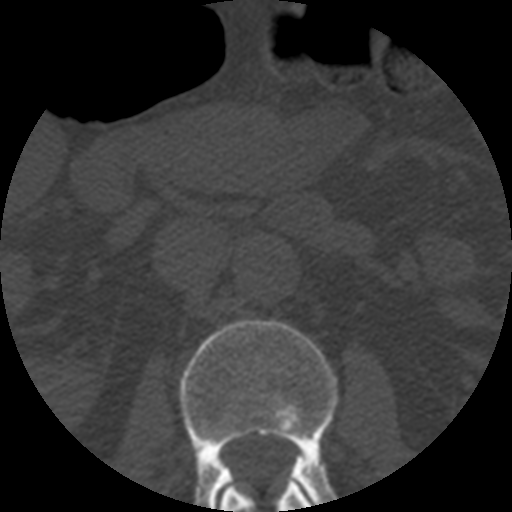
CT including the spine, one axial slice; slice 162 of 508 in the series (ordered by position); reconstruction kernel STANDARD; bone window (W 1800 / L 400 HU); 1.25 mm slice thickness; 512 × 512 image matrix, field of view 160 × 160 mm. Patient age 57 years. From the clinical record (not read from this slice): primary cancer: prostate.
Outlined on this slice (semi-automatically segmented with operator editing):
- L1 vertebra: box from (x=220, y=482) to (x=314, y=512) px
- L2 vertebra: (x=179, y=320)–(x=338, y=512)